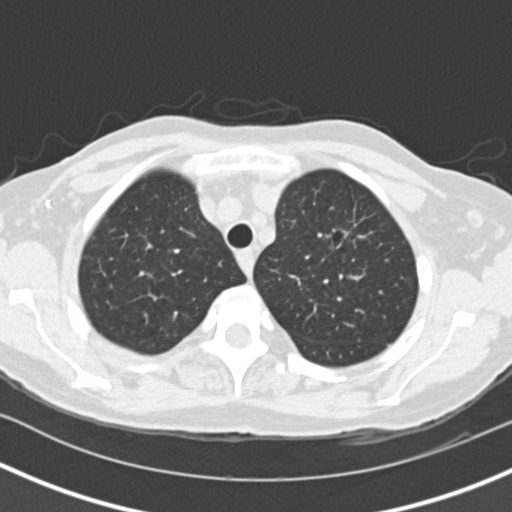
Low-dose screening chest CT, axial slice, baseline screening round, lung window (W 1500 / L -600 HU), 2 mm slice thickness, 512 × 512 image matrix, field of view 310 × 310 mm. Female participant, aged 73 years at enrolment. Current smoker at enrolment.
Lesion marked by an expert reader, bounding box <314,213,368,279> (left, top, right, bottom; pixels). Reader record for this screening exam (exam-level; its link to the box is not recorded): non-calcified nodule or mass ≥4 mm, left upper lobe, 27 × 21 mm, spiculated (stellate) margins, soft tissue attenuation. Official screen result: positive, change unspecified: nodule(s) >= 4 mm or enlarging nodule(s), mass(es), or other non-specific abnormalities suspicious for lung cancer. Later outcome: lung cancer diagnosed 72 days after this screen — bronchiolo-alveolar adenocarcinoma, NOS, left upper lobe, moderately differentiated (G2), stage IIIB (AJCC 6th edition), 17 mm at pathology.